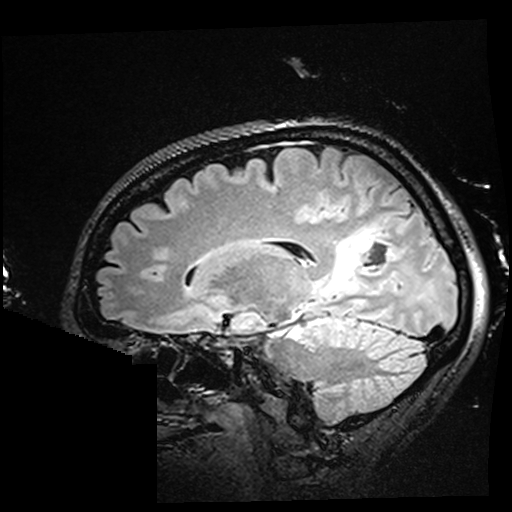
Brain MRI from a brain-tumour surgery series, one sagittal slice; slice 107 of 176 in the series (ordered by position); T2 FLAIR; 512 × 512 image matrix. From the clinical record (not read from this slice): histopathology: Oligodendroglioma; WHO grade: 2; IDH mutation: yes; tumour location: Right Parietal.
Outlined on this slice (outlined manually by an expert reader):
- residual tumour: bounding box [x1, y1, x2, y2] px = [323, 229, 374, 297]